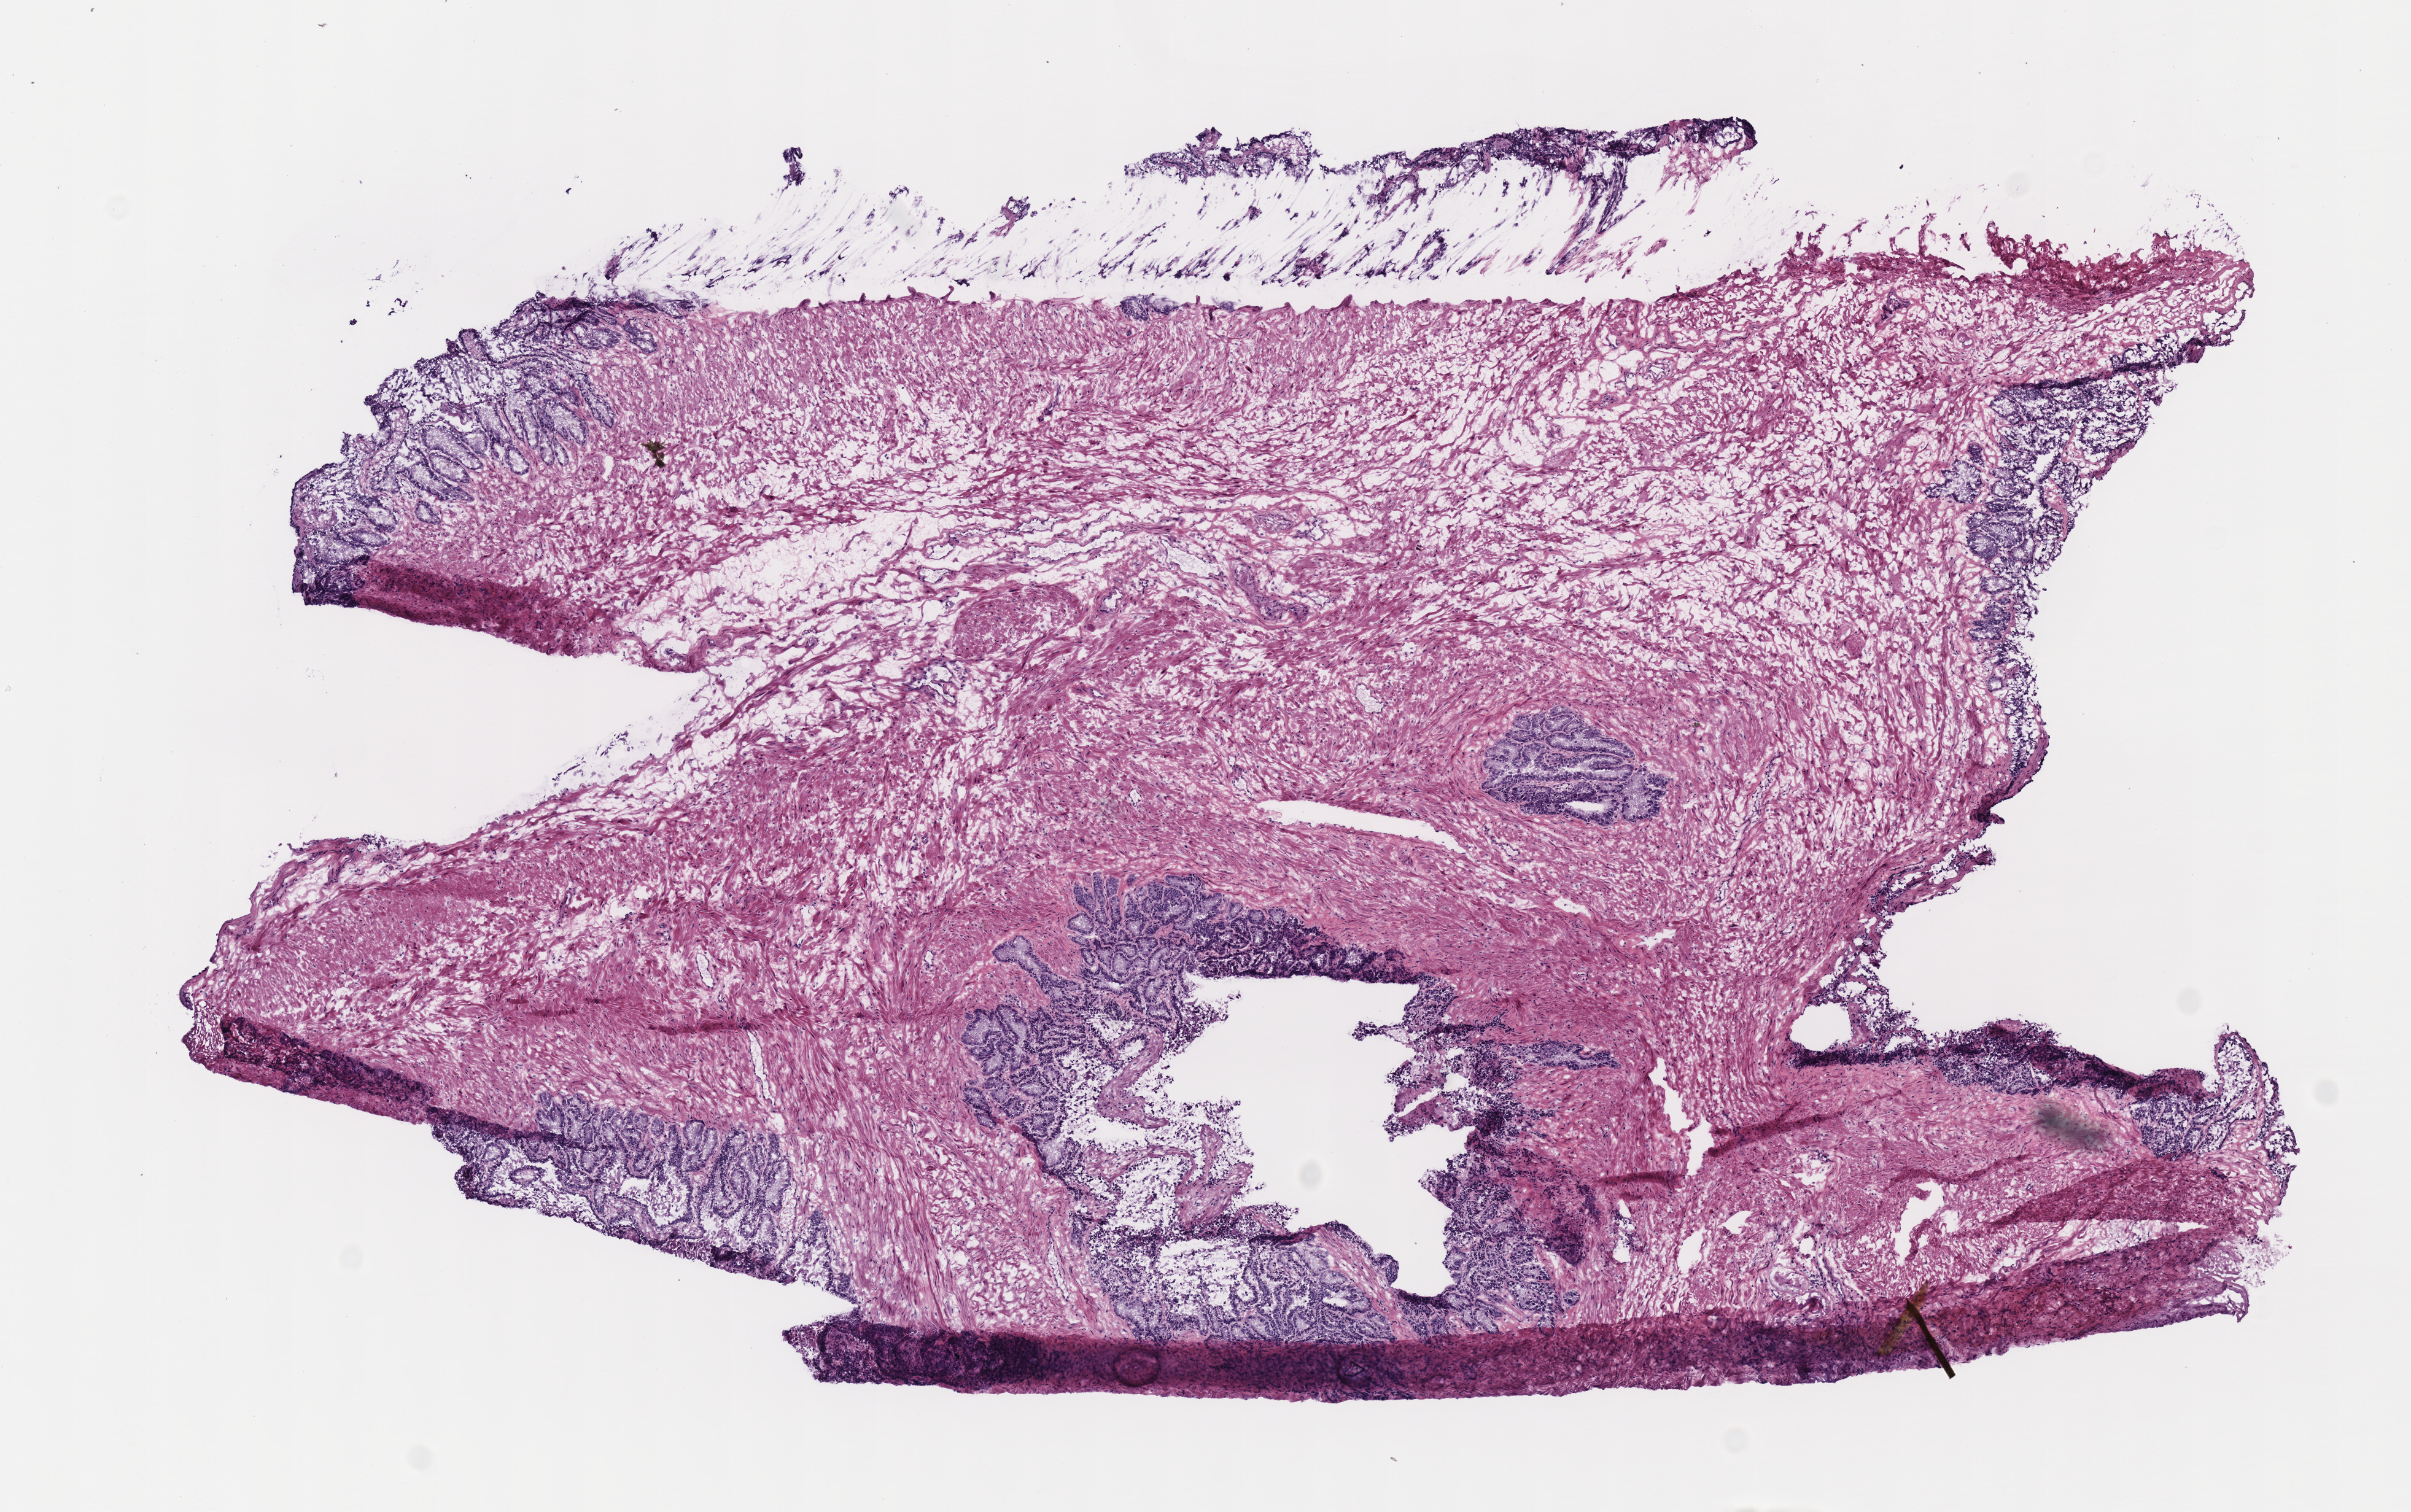
Digitized H&E tissue section (whole slide), a low-resolution overview of the entire scanned area, about 7.7 x 4.9 mm (from a 40x scan), frozen section, solid tissue normal (non-tumour tissue) sample from the prostate. Male patient; age at initial diagnosis 56 years.
This section: solid tissue normal sample (biorepository sample class). Patient diagnosis: Acinar cell carcinoma (prostate gland).